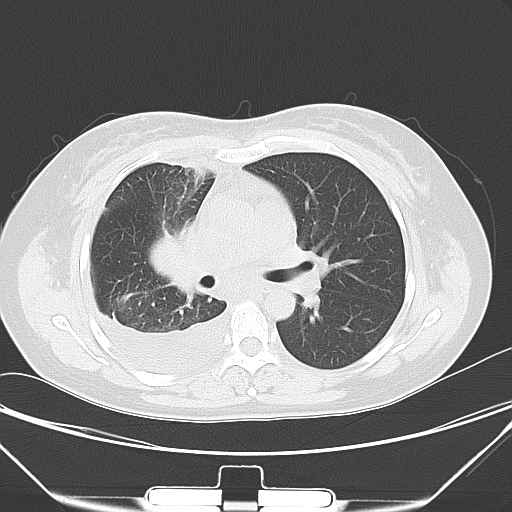
Chest CT, one axial slice. Slice 31 of 52 in the series (ordered by position). 120 kVp. Lung window (W 1500 / L -600 HU). 5 mm slice thickness. 512 × 512 image matrix, field of view 352 × 352 mm. Female patient, age 36 years. From the clinical record (not read from this slice): clinical TNM (as recorded): T1b N2 M0; histopathological grade: G3.
Outlined on this slice (rectangle marked by the reading radiologist):
- lung tumour (recorded histology: adenocarcinoma): box from (x=145, y=219) to (x=204, y=298) px